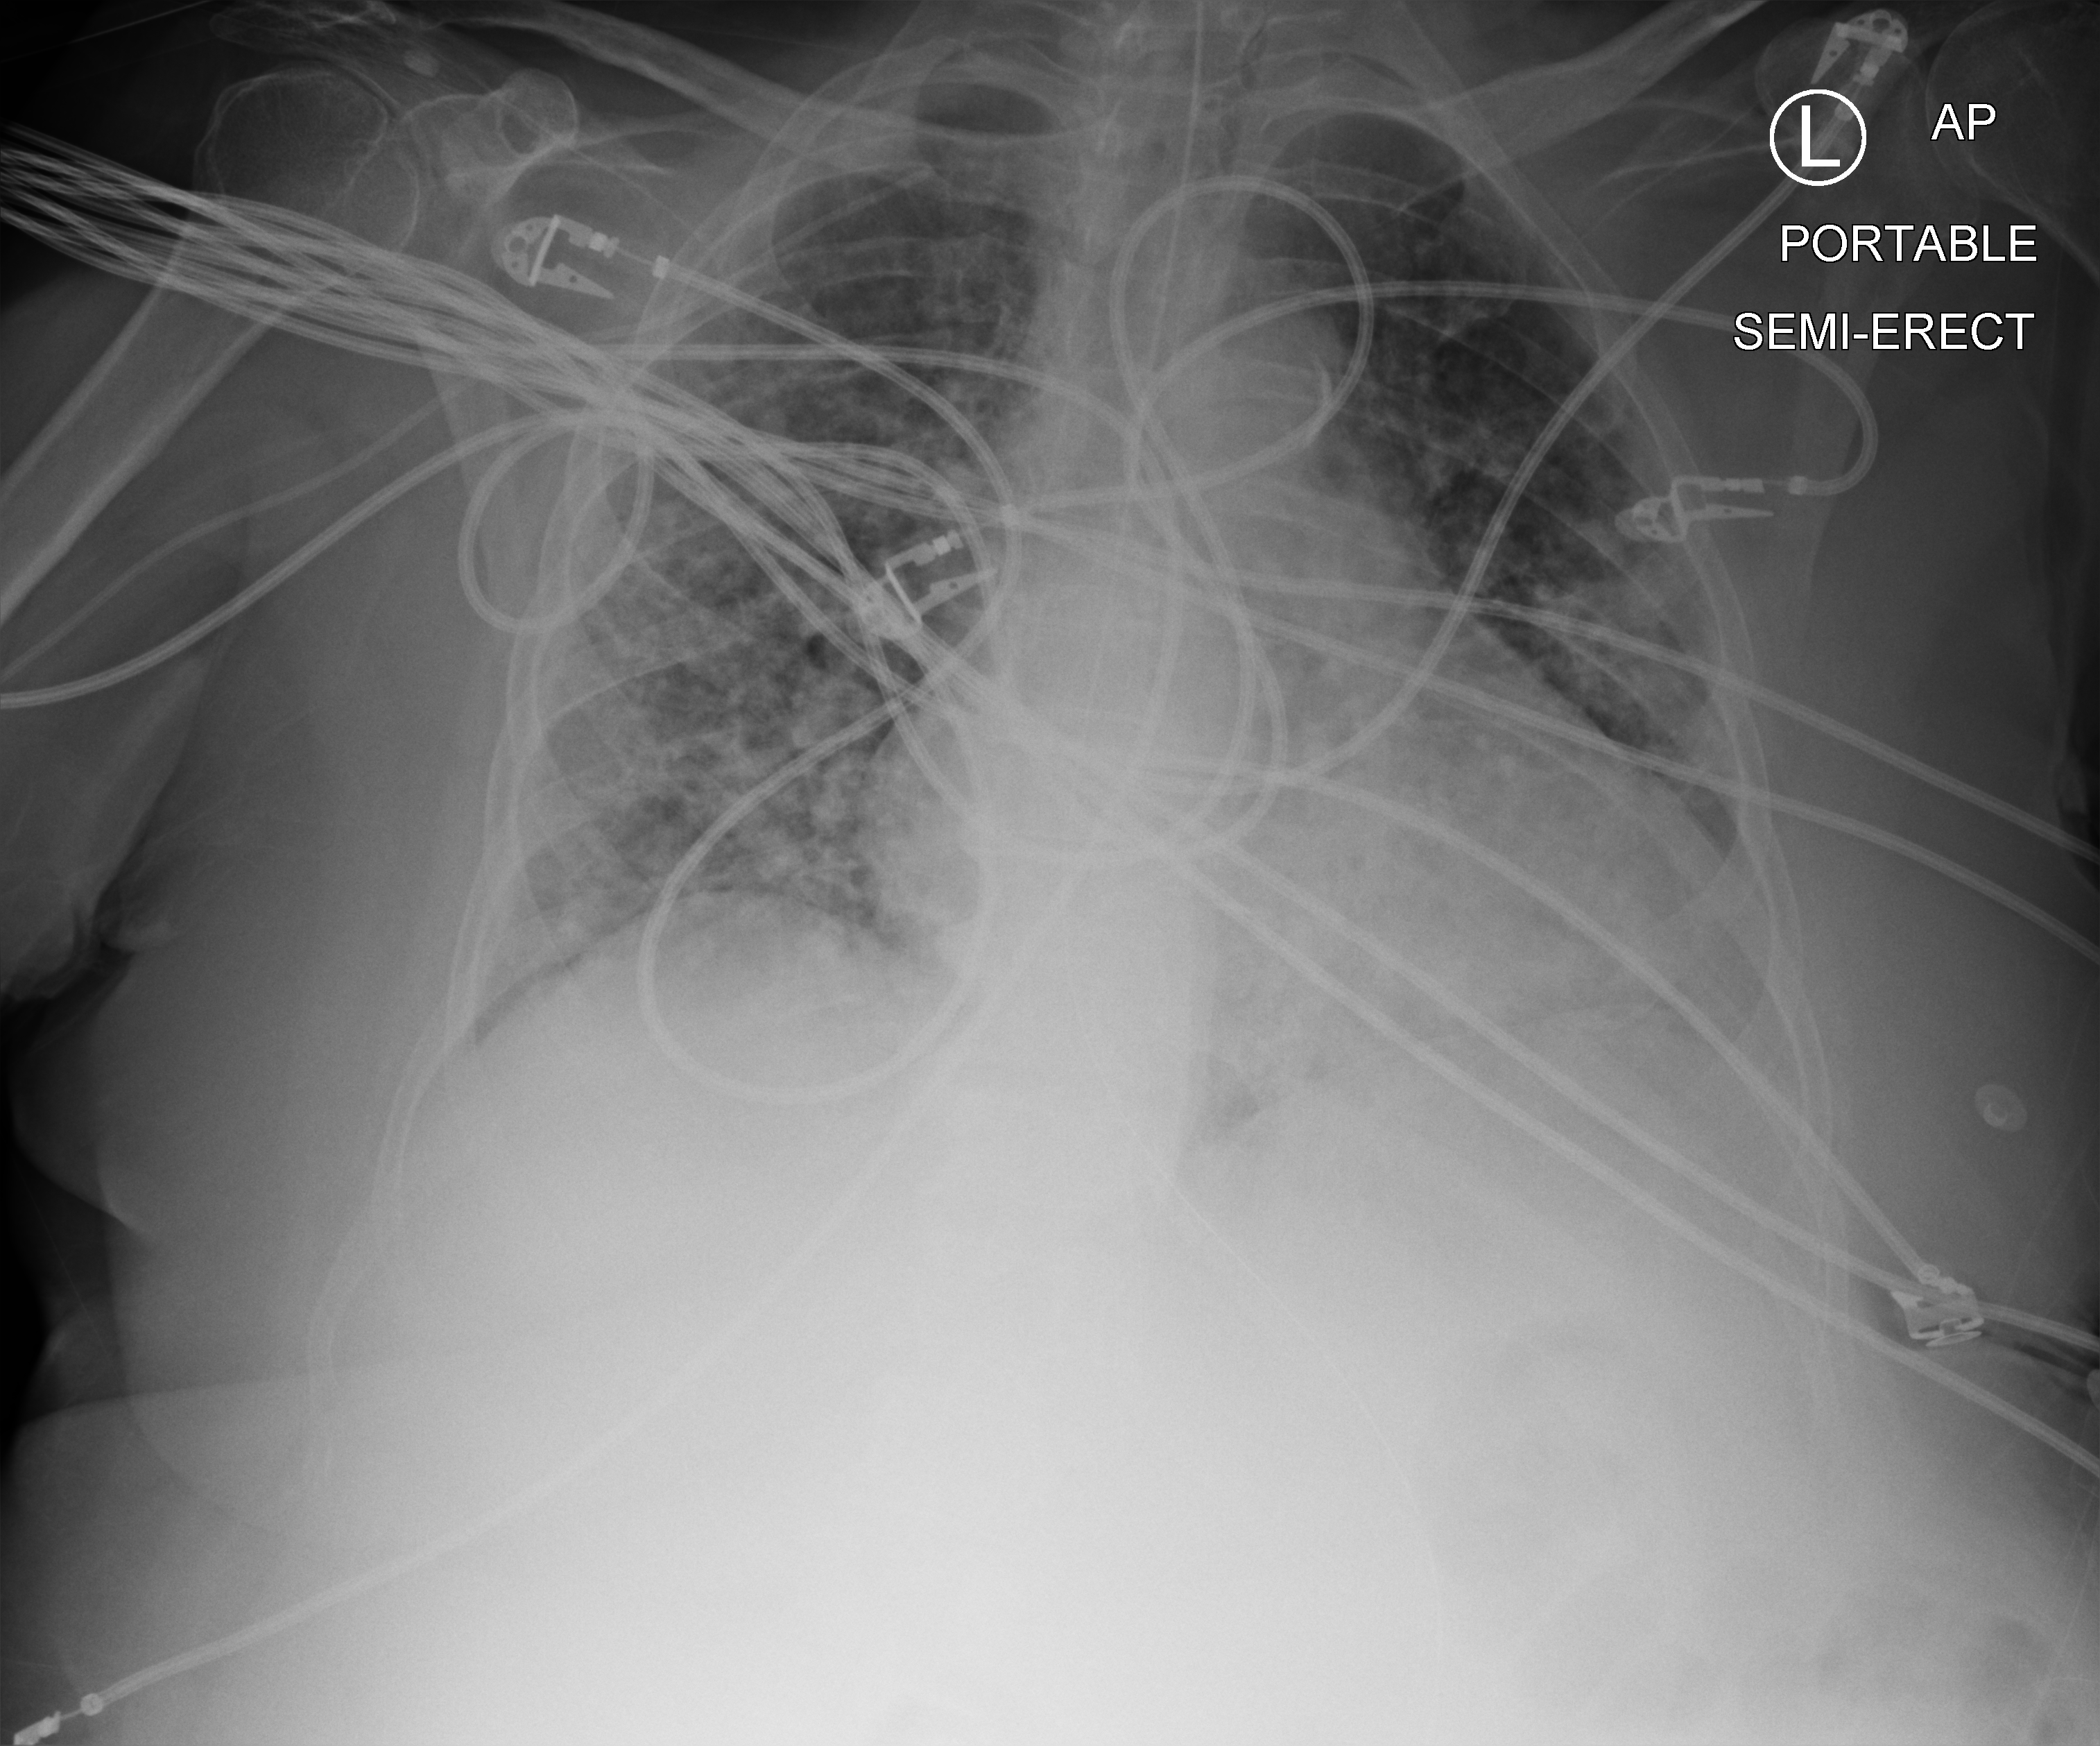
Chest X-ray (portable); anteroposterior (AP) projection. Female patient hospitalised with COVID-19, age 75–90 years.
Hospital-stay facts (about this admission, not read from this image; timing relative to this image not recorded): length of hospital stay: 31 days; mechanically ventilated during this hospital stay: yes.